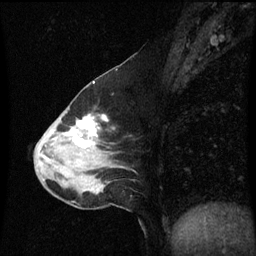
Breast MRI (dynamic contrast-enhanced), one sagittal slice. Dynamic contrast-enhanced series, image 2 of 3 at this slice position (ordered by acquisition). 1.5 T. TE 4.2 ms, TR 8.9 ms. 2 mm slice thickness. 256 × 256 image matrix, field of view 200 × 200 mm. Female patient, age 50 years. From the clinical record (not read from this slice): setting: breast cancer imaged before/during neoadjuvant chemotherapy; receptor status: HR-positive, HER2-negative.
Outlined on this slice (semi-automatic segmentation, software-assisted and operator-edited):
- analysis volume of interest (the breast-tissue region the enhancement analysis was run in; not a lesion): bounding box [x1, y1, x2, y2] px = [36, 90, 127, 209]
- tumour enhancement mask (voxels above the 70 % enhancement threshold inside the analysis volume of interest): [68, 116, 108, 147]